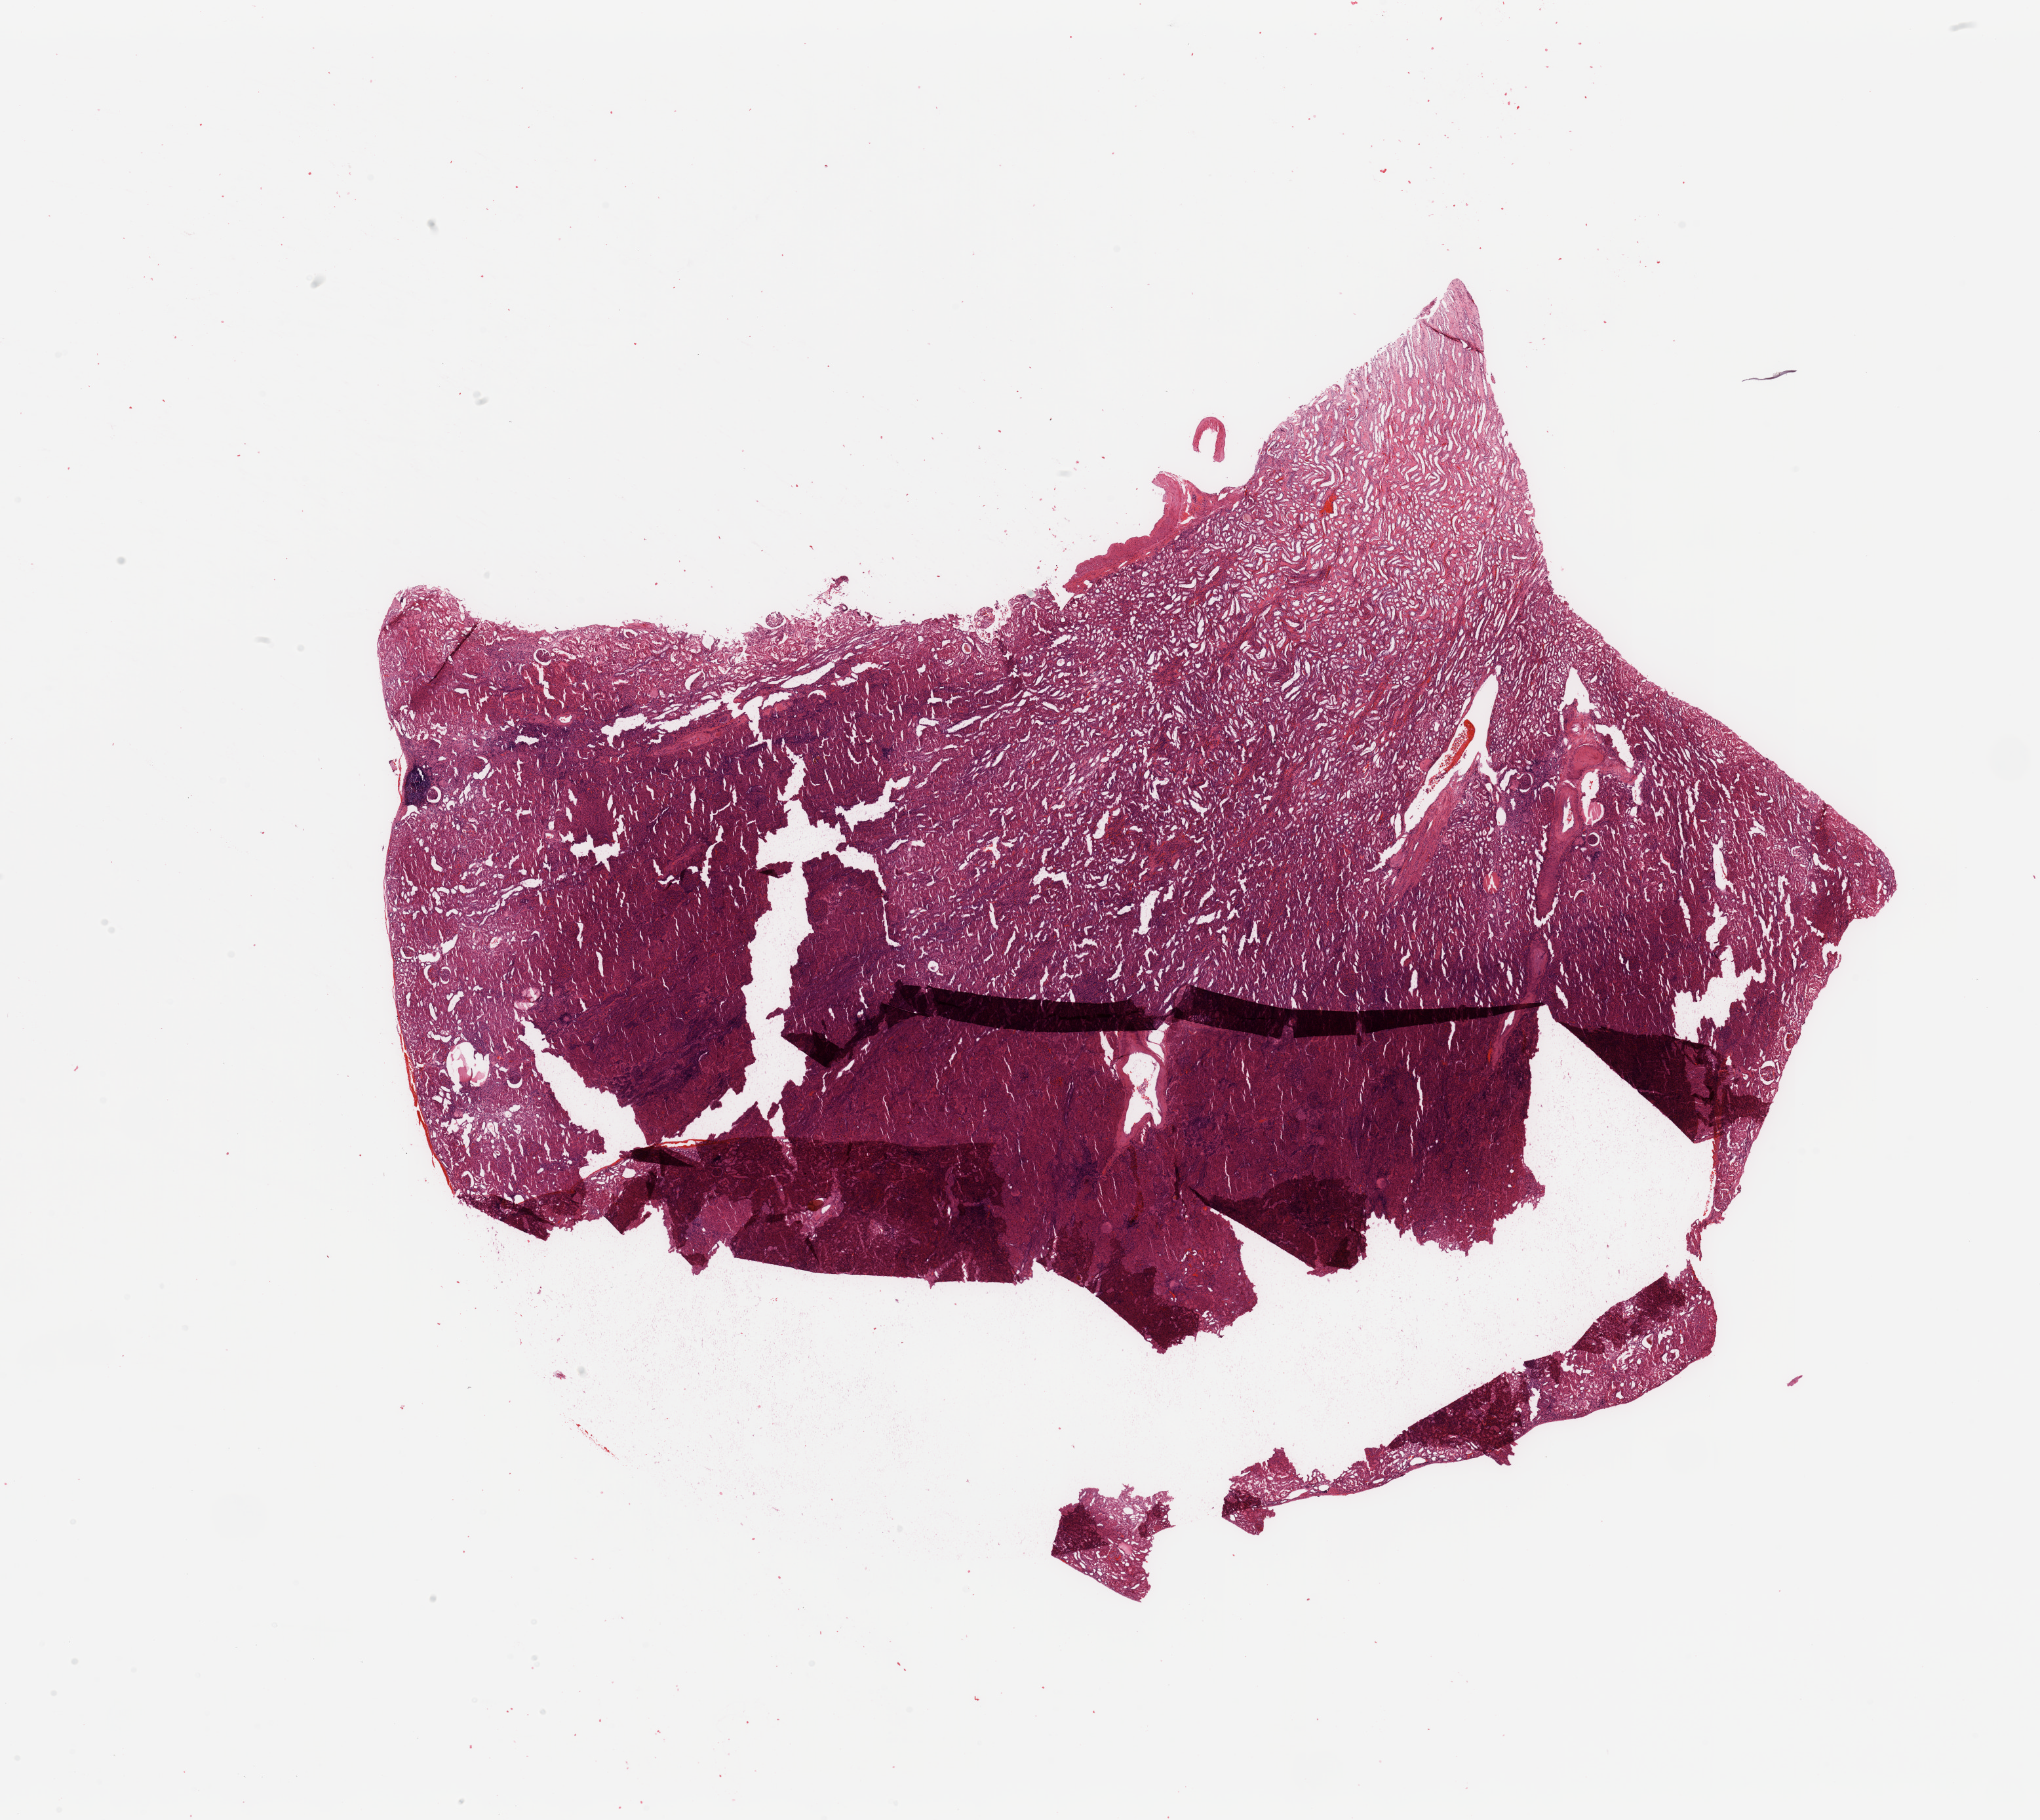
Digitized H&E tissue section (whole slide) — a low-resolution overview of the entire scanned area, about 24.6 x 22.0 mm, normal (non-tumour) tissue sample, kidney. Male, 53 y/o.
This section: normal (non-tumour) tissue from the same patient. Patient diagnosis: Renal cell carcinoma, NOS.